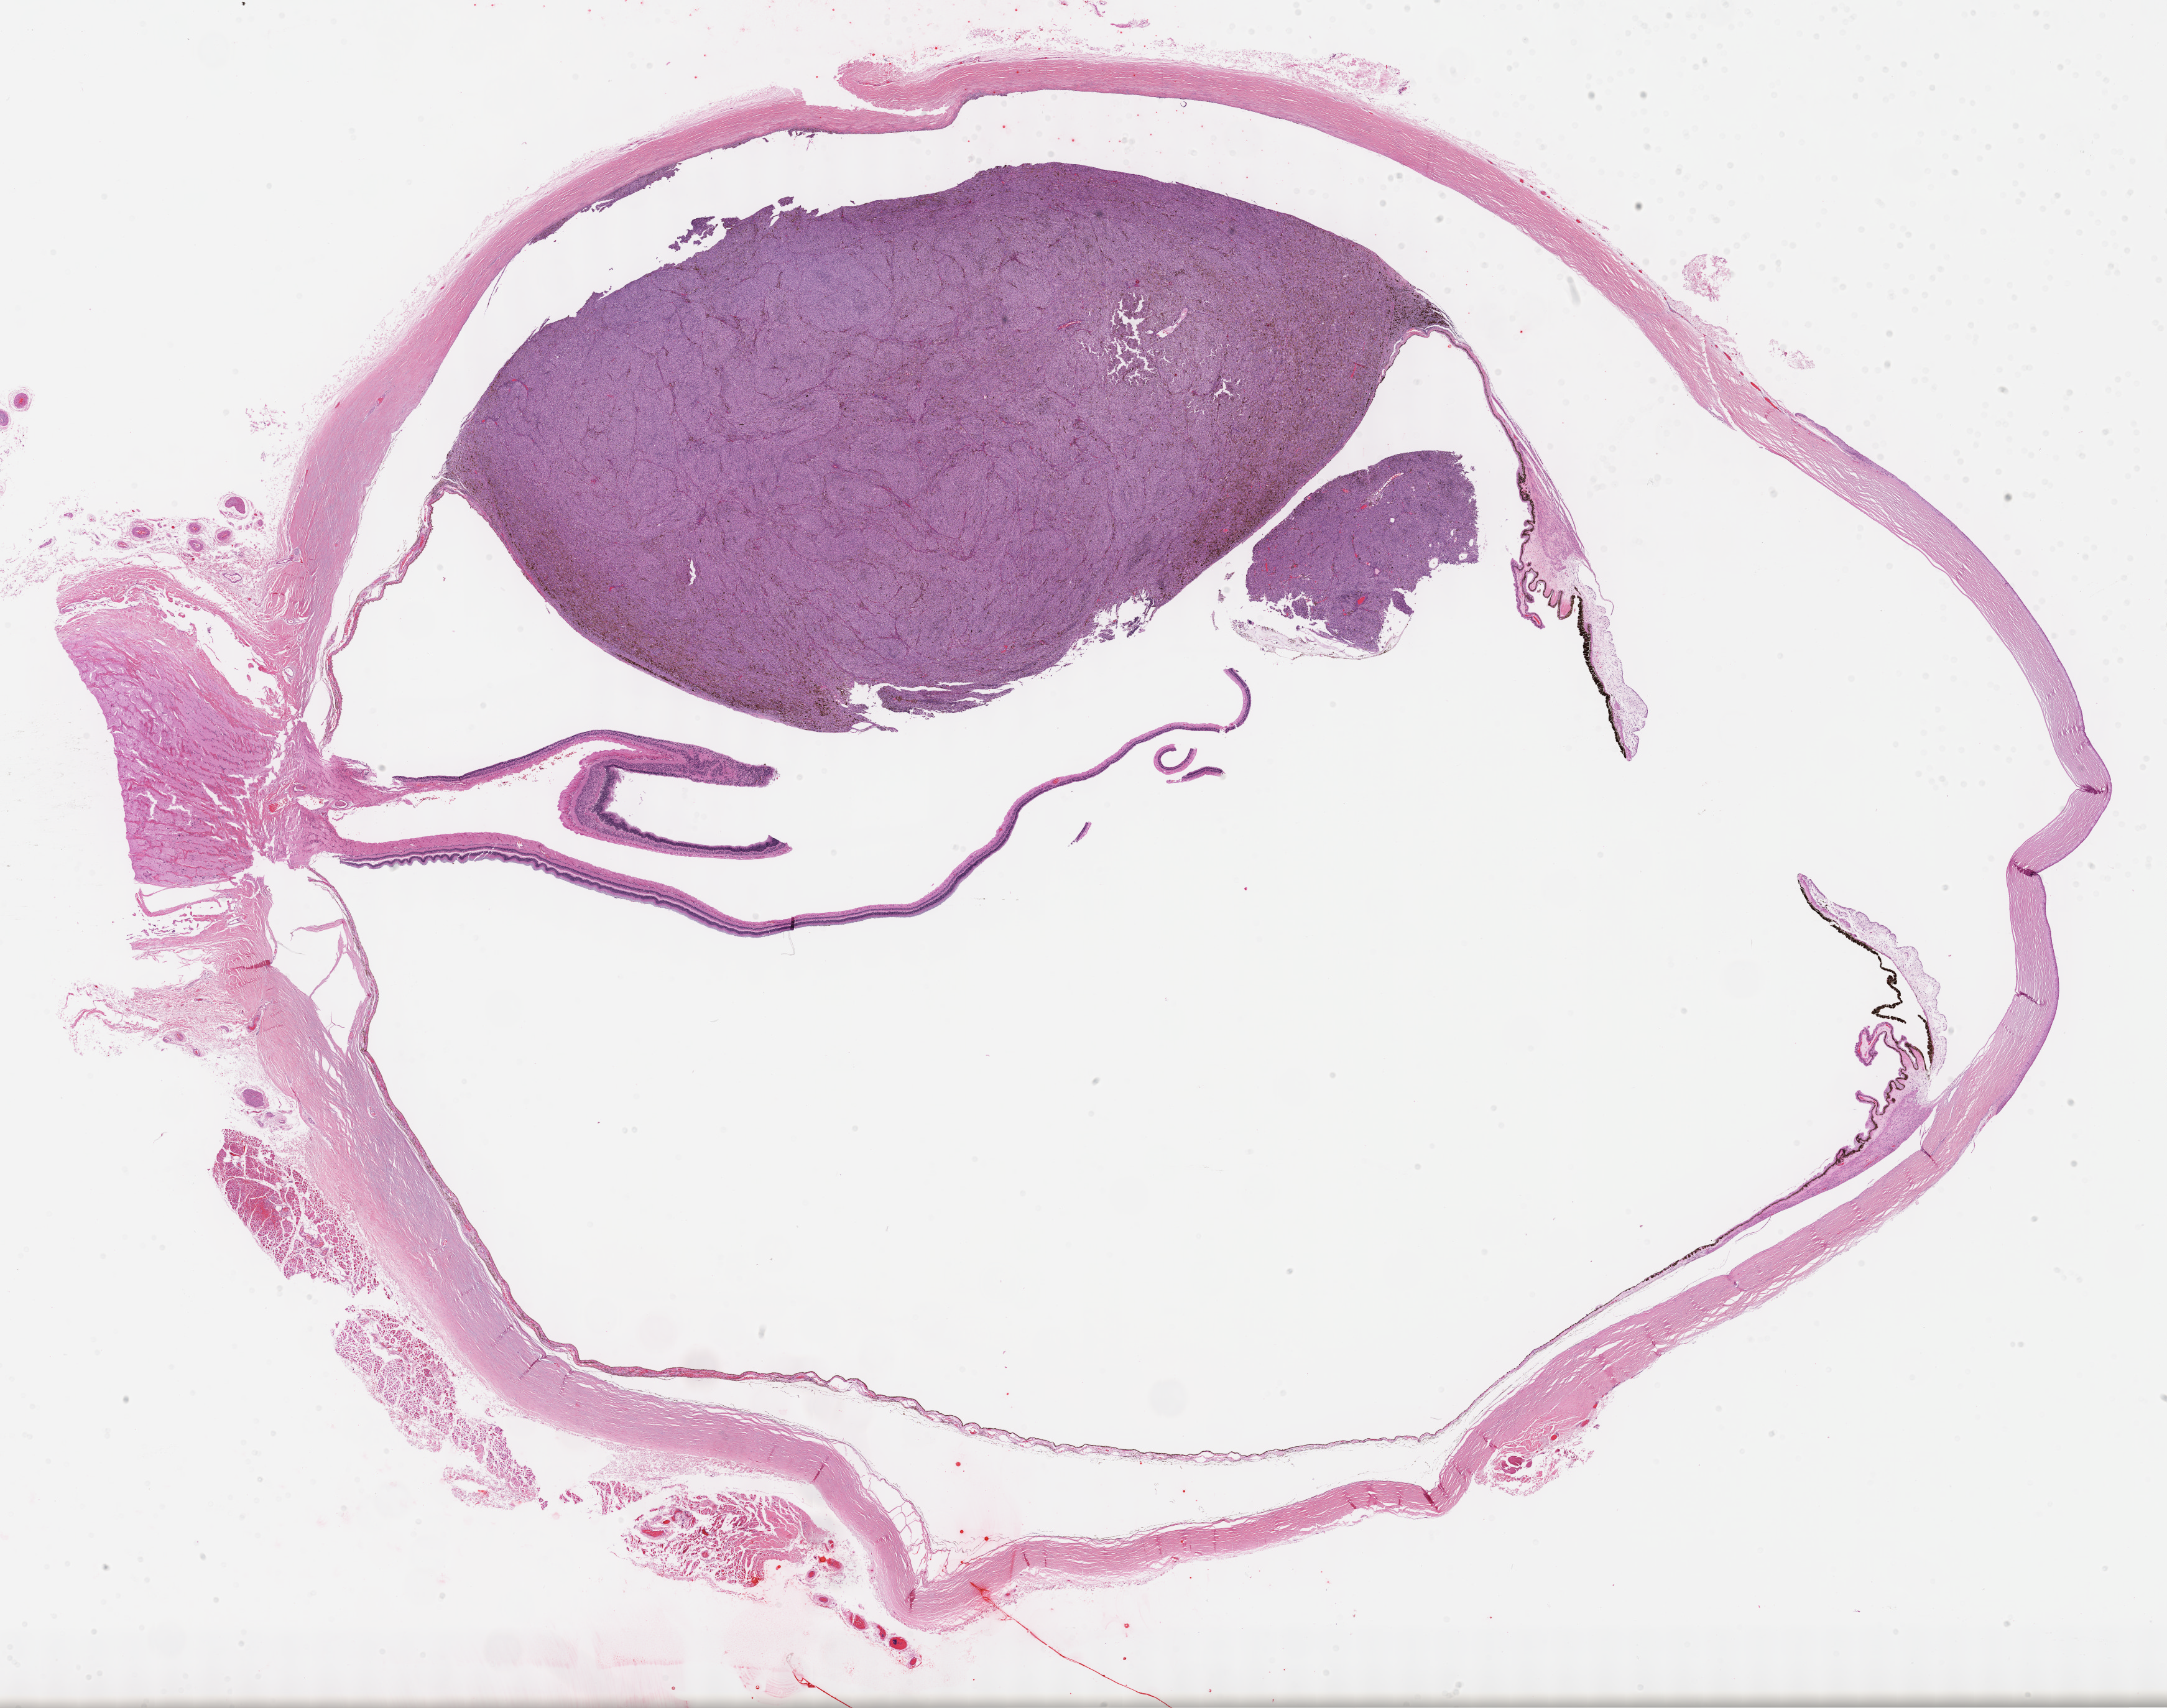
Digitized H&E tissue section (whole slide) — whole scanned area (about 28.2 x 22.2 mm, acquisition: 40x scan) shown as a low-resolution overview; formalin-fixed paraffin-embedded (FFPE) diagnostic section; primary tumour sample from the uvea. Male patient; age at initial diagnosis 59 years.
Histologic diagnosis: Mixed epithelioid and spindle cell melanoma (choroid). Laterality: right.